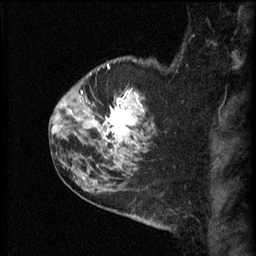
Breast MRI (dynamic contrast-enhanced), one sagittal slice. Slice 47 of 60 in the series (ordered by position). 3 images stored at this slice position (order not interpretable as contrast timing). 1.5 T. TE 4.2 ms, TR 11 ms. 256 × 256 image matrix, field of view 180 × 180 mm. Female patient, age 52 years.
Structures marked on this image (semi-automatically segmented with operator editing):
- analysis volume of interest (the breast-tissue region the enhancement analysis was run in; not a lesion): bounding box [x1, y1, x2, y2] px = [86, 76, 157, 157]
- tumour enhancement mask (voxels above the 70 % enhancement threshold inside the analysis volume of interest): [94, 90, 144, 149]